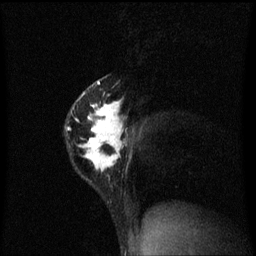
Breast MRI (dynamic contrast-enhanced), one sagittal slice. Slice 42 of 60 in the series (ordered by position). Dynamic contrast-enhanced series, image 2 of 3 at this slice position (ordered by acquisition). 1.5 T. TE 4.2 ms, TR 8.4 ms. 2 mm slice thickness. 256 × 256 image matrix, field of view 200 × 200 mm. Female patient, age 40 years.
Structures marked on this image (semi-automatically segmented with operator editing):
- analysis volume of interest (the breast-tissue region the enhancement analysis was run in; not a lesion): bounding box [x1, y1, x2, y2] px = [66, 76, 126, 189]
- tumour enhancement mask (voxels above the 70 % enhancement threshold inside the analysis volume of interest): [66, 82, 126, 173]